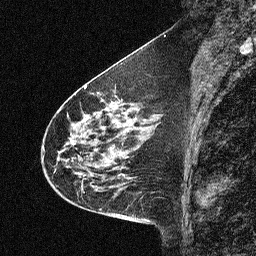
Breast MRI (dynamic contrast-enhanced), one sagittal slice. Dynamic contrast-enhanced study with each time point stored as its own series, time point 2 of 3 at this slice position (early post-contrast, ordered by acquisition time). 1.5 T. TE 4.5 ms, TR 11 ms. 2.06 mm slice thickness. 256 × 256 image matrix, field of view 200 × 200 mm. Female patient, age 46 years. From the clinical record (not read from this slice): setting: breast cancer imaged before/during neoadjuvant chemotherapy; receptor status: HER2-positive.
Structures marked on this image (semi-automatic segmentation, software-assisted and operator-edited):
- analysis volume of interest (the breast-tissue region the enhancement analysis was run in; not a lesion): bounding box [x1, y1, x2, y2] px = [42, 80, 150, 180]
- tumour enhancement mask (voxels above the 90 % enhancement threshold inside the analysis volume of interest): [58, 100, 134, 177]